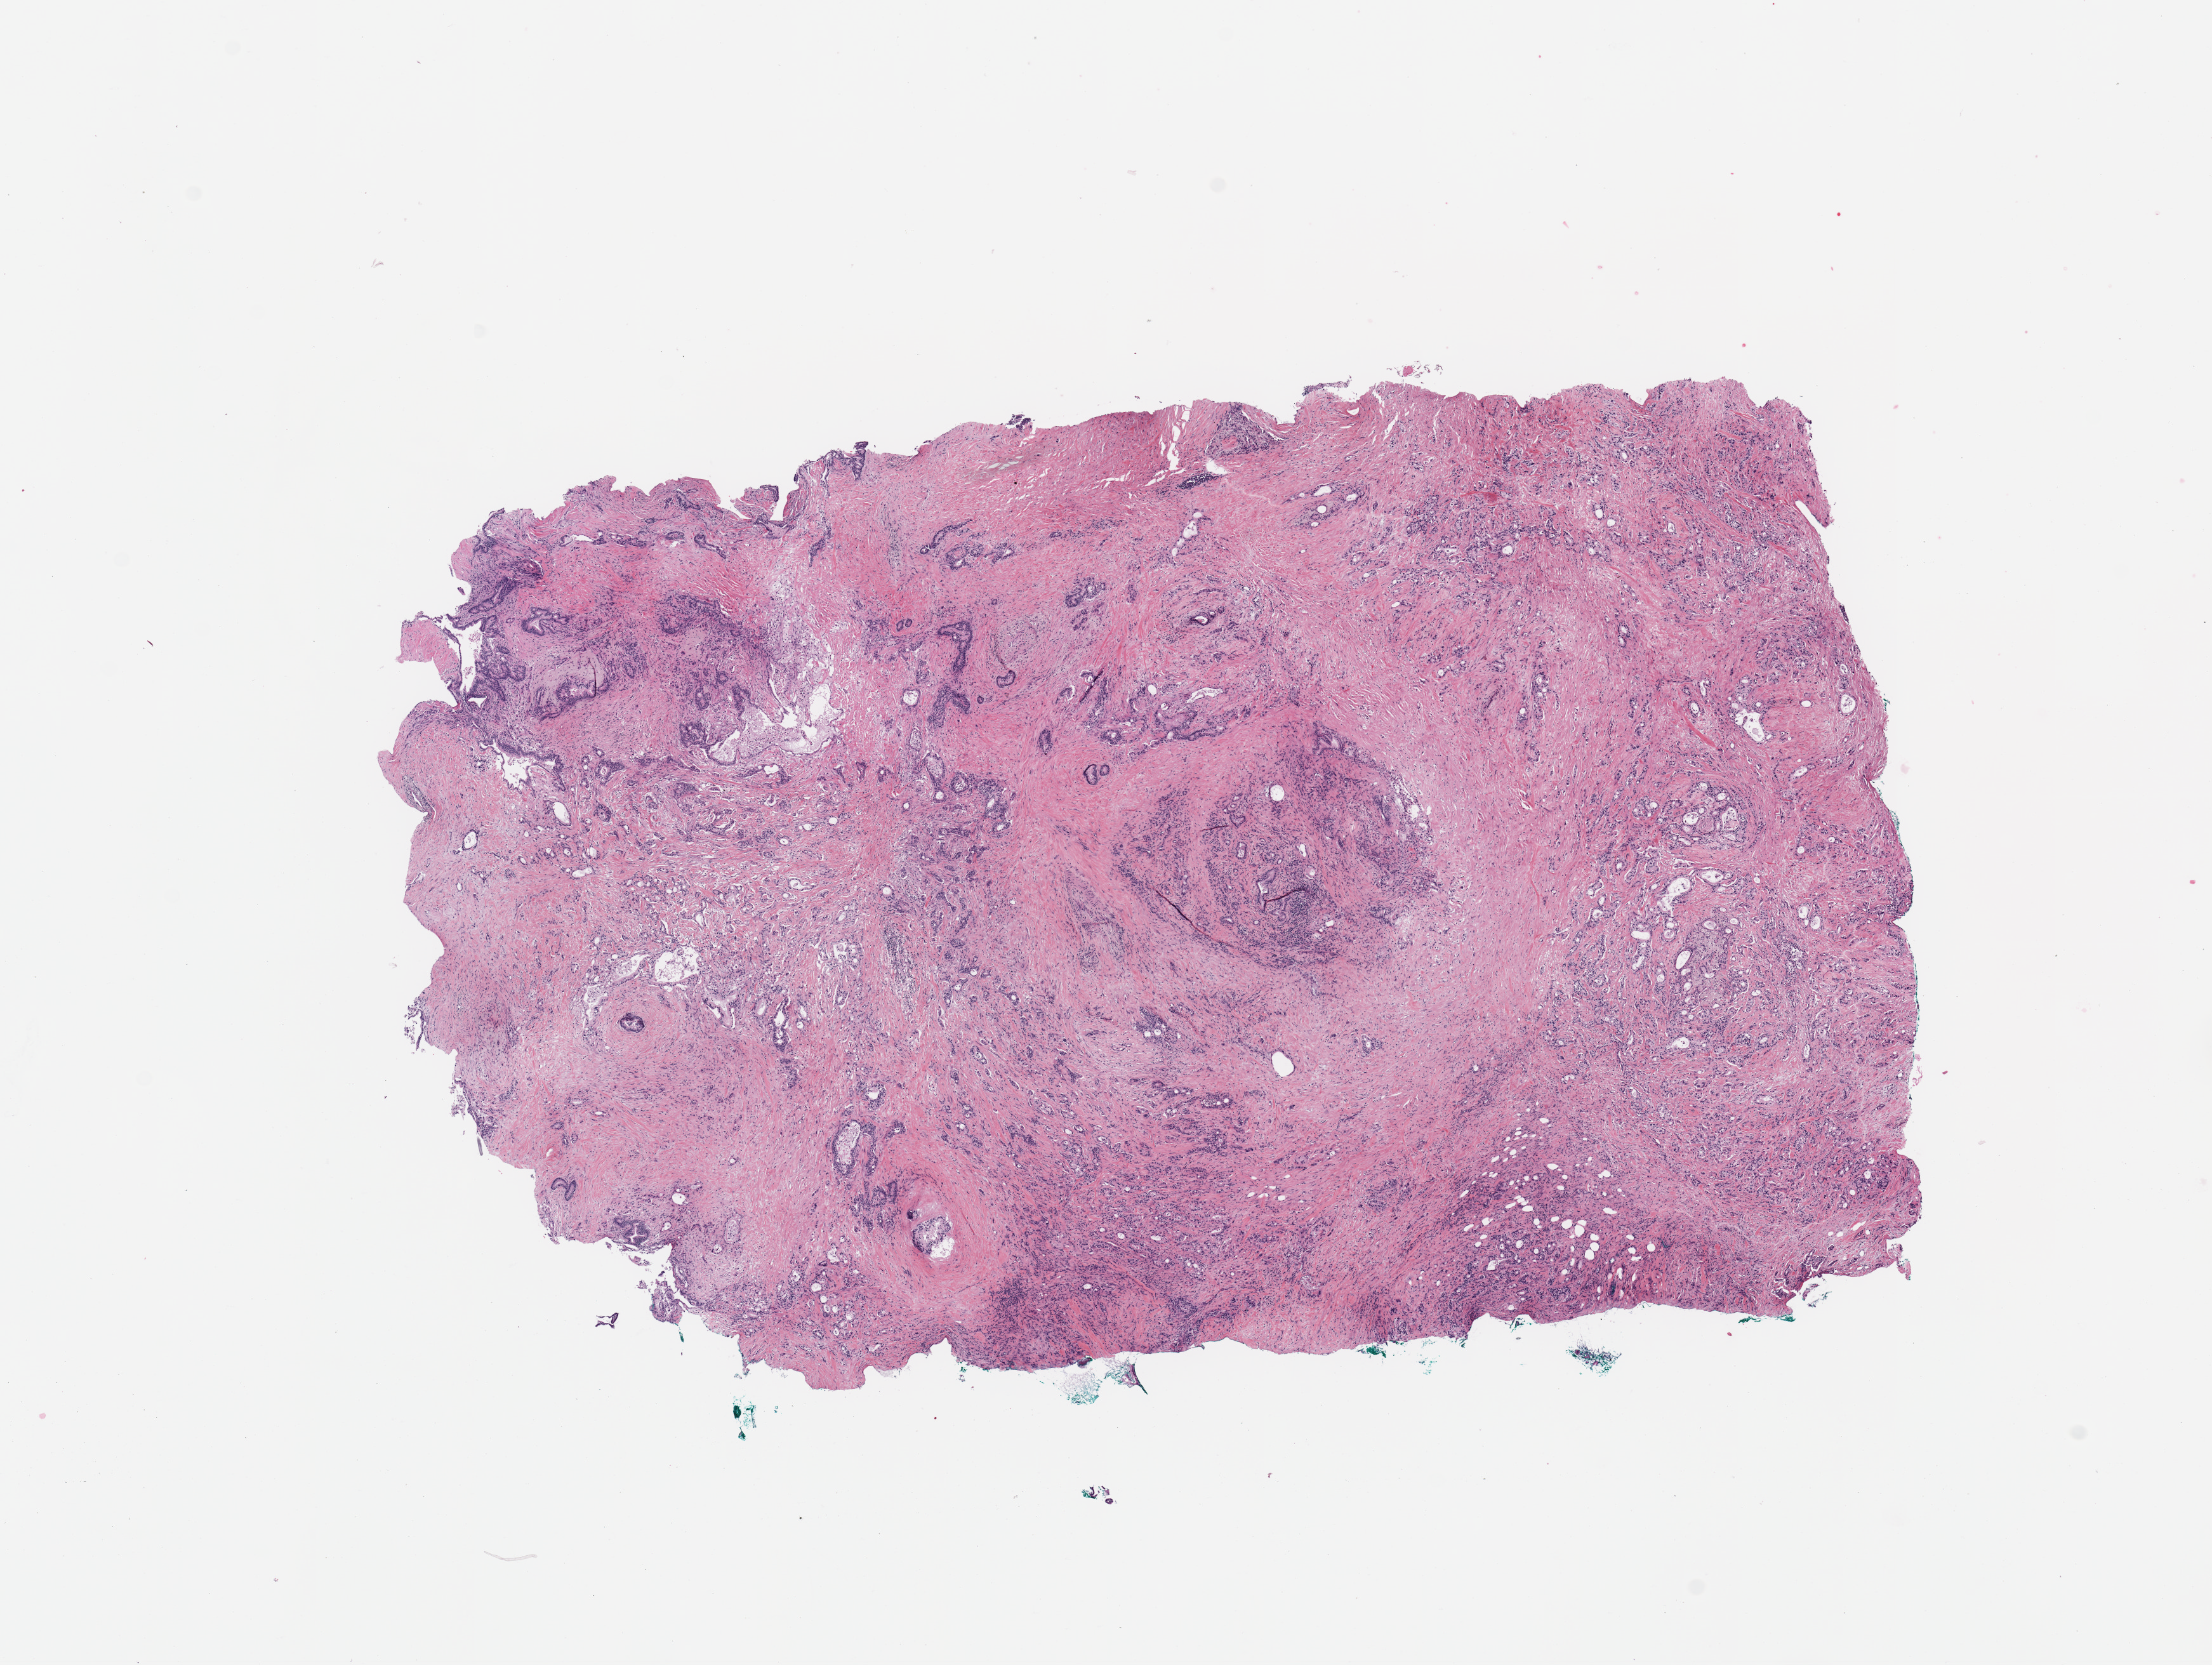
Digitized Hematoxylin and eosin (H&E) stained tissue section (whole slide) — low-resolution overview of the scanned area, about 13.8 x 10.4 mm, pancreas, tumour tissue. 64-year-old male patient. Histologic grade: G2 (moderately differentiated).
• AJCC pathologic stage: IIB
• primary tumour site (as recorded): head
• histologic diagnosis: Infiltrating duct carcinoma, NOS